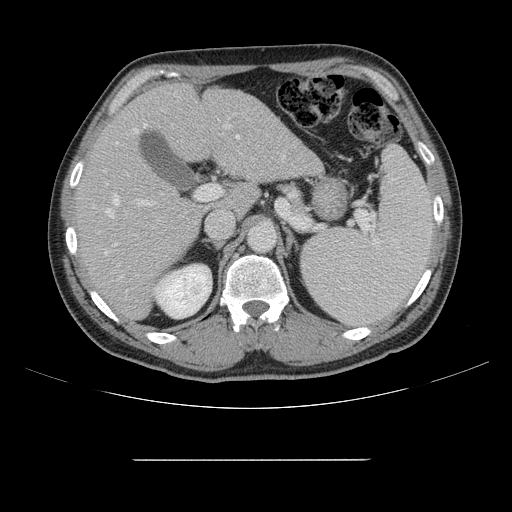
Contrast-enhanced abdominal CT, one axial slice. Position 95 of 164 along the scan axis. 120 kVp. Intravenous contrast given. Soft-tissue window (W 400 / L 40 HU). 2.5 mm slice thickness. 512 × 512 image matrix, field of view 404 × 404 mm. Male patient, age 54 years. Case-level facts recorded for this patient, not image findings: diagnosis: colorectal cancer liver metastases, imaged before liver resection; multiple liver metastases: yes; largest metastasis: 1 cm; chemotherapy before resection: yes.
Structures marked on this image (manually delineated by an expert):
- hepatic veins: bounding box <105,128,284,278> (left, top, right, bottom; pixels)
- liver: <78,84,320,320>
- planned liver remnant (the part of the liver to remain after resection): <77,84,234,319>
- portal vein (with intrahepatic branches): <116,93,231,205>